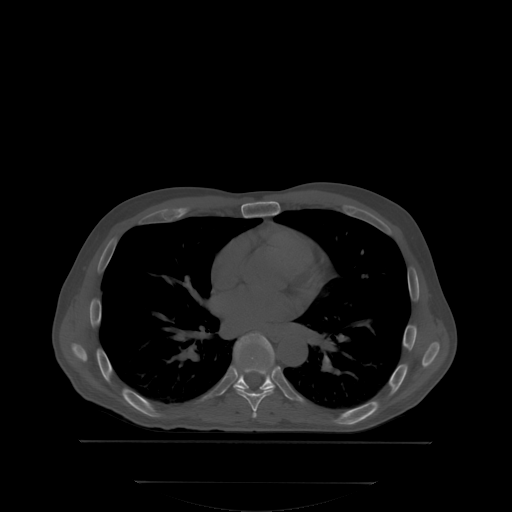
CT including the spine, one axial slice; position 222 of 350 along the scan axis; bone window (W 1800 / L 400 HU); 2.5 mm slice thickness; 512 × 512 image matrix, field of view 500 × 500 mm. Male patient, age 58 years. Case-level facts recorded for this patient, not image findings: primary cancer: prostate; vertebrae with lytic lesions (as recorded): L1.
Outlined on this slice (semi-automatically segmented with operator editing):
- T6 vertebra: bounding box (x1, y1, x2, y2) in pixels: (253, 412, 256, 416)
- T7 vertebra: (233, 365, 274, 412)
- T8 vertebra: (210, 334, 274, 395)